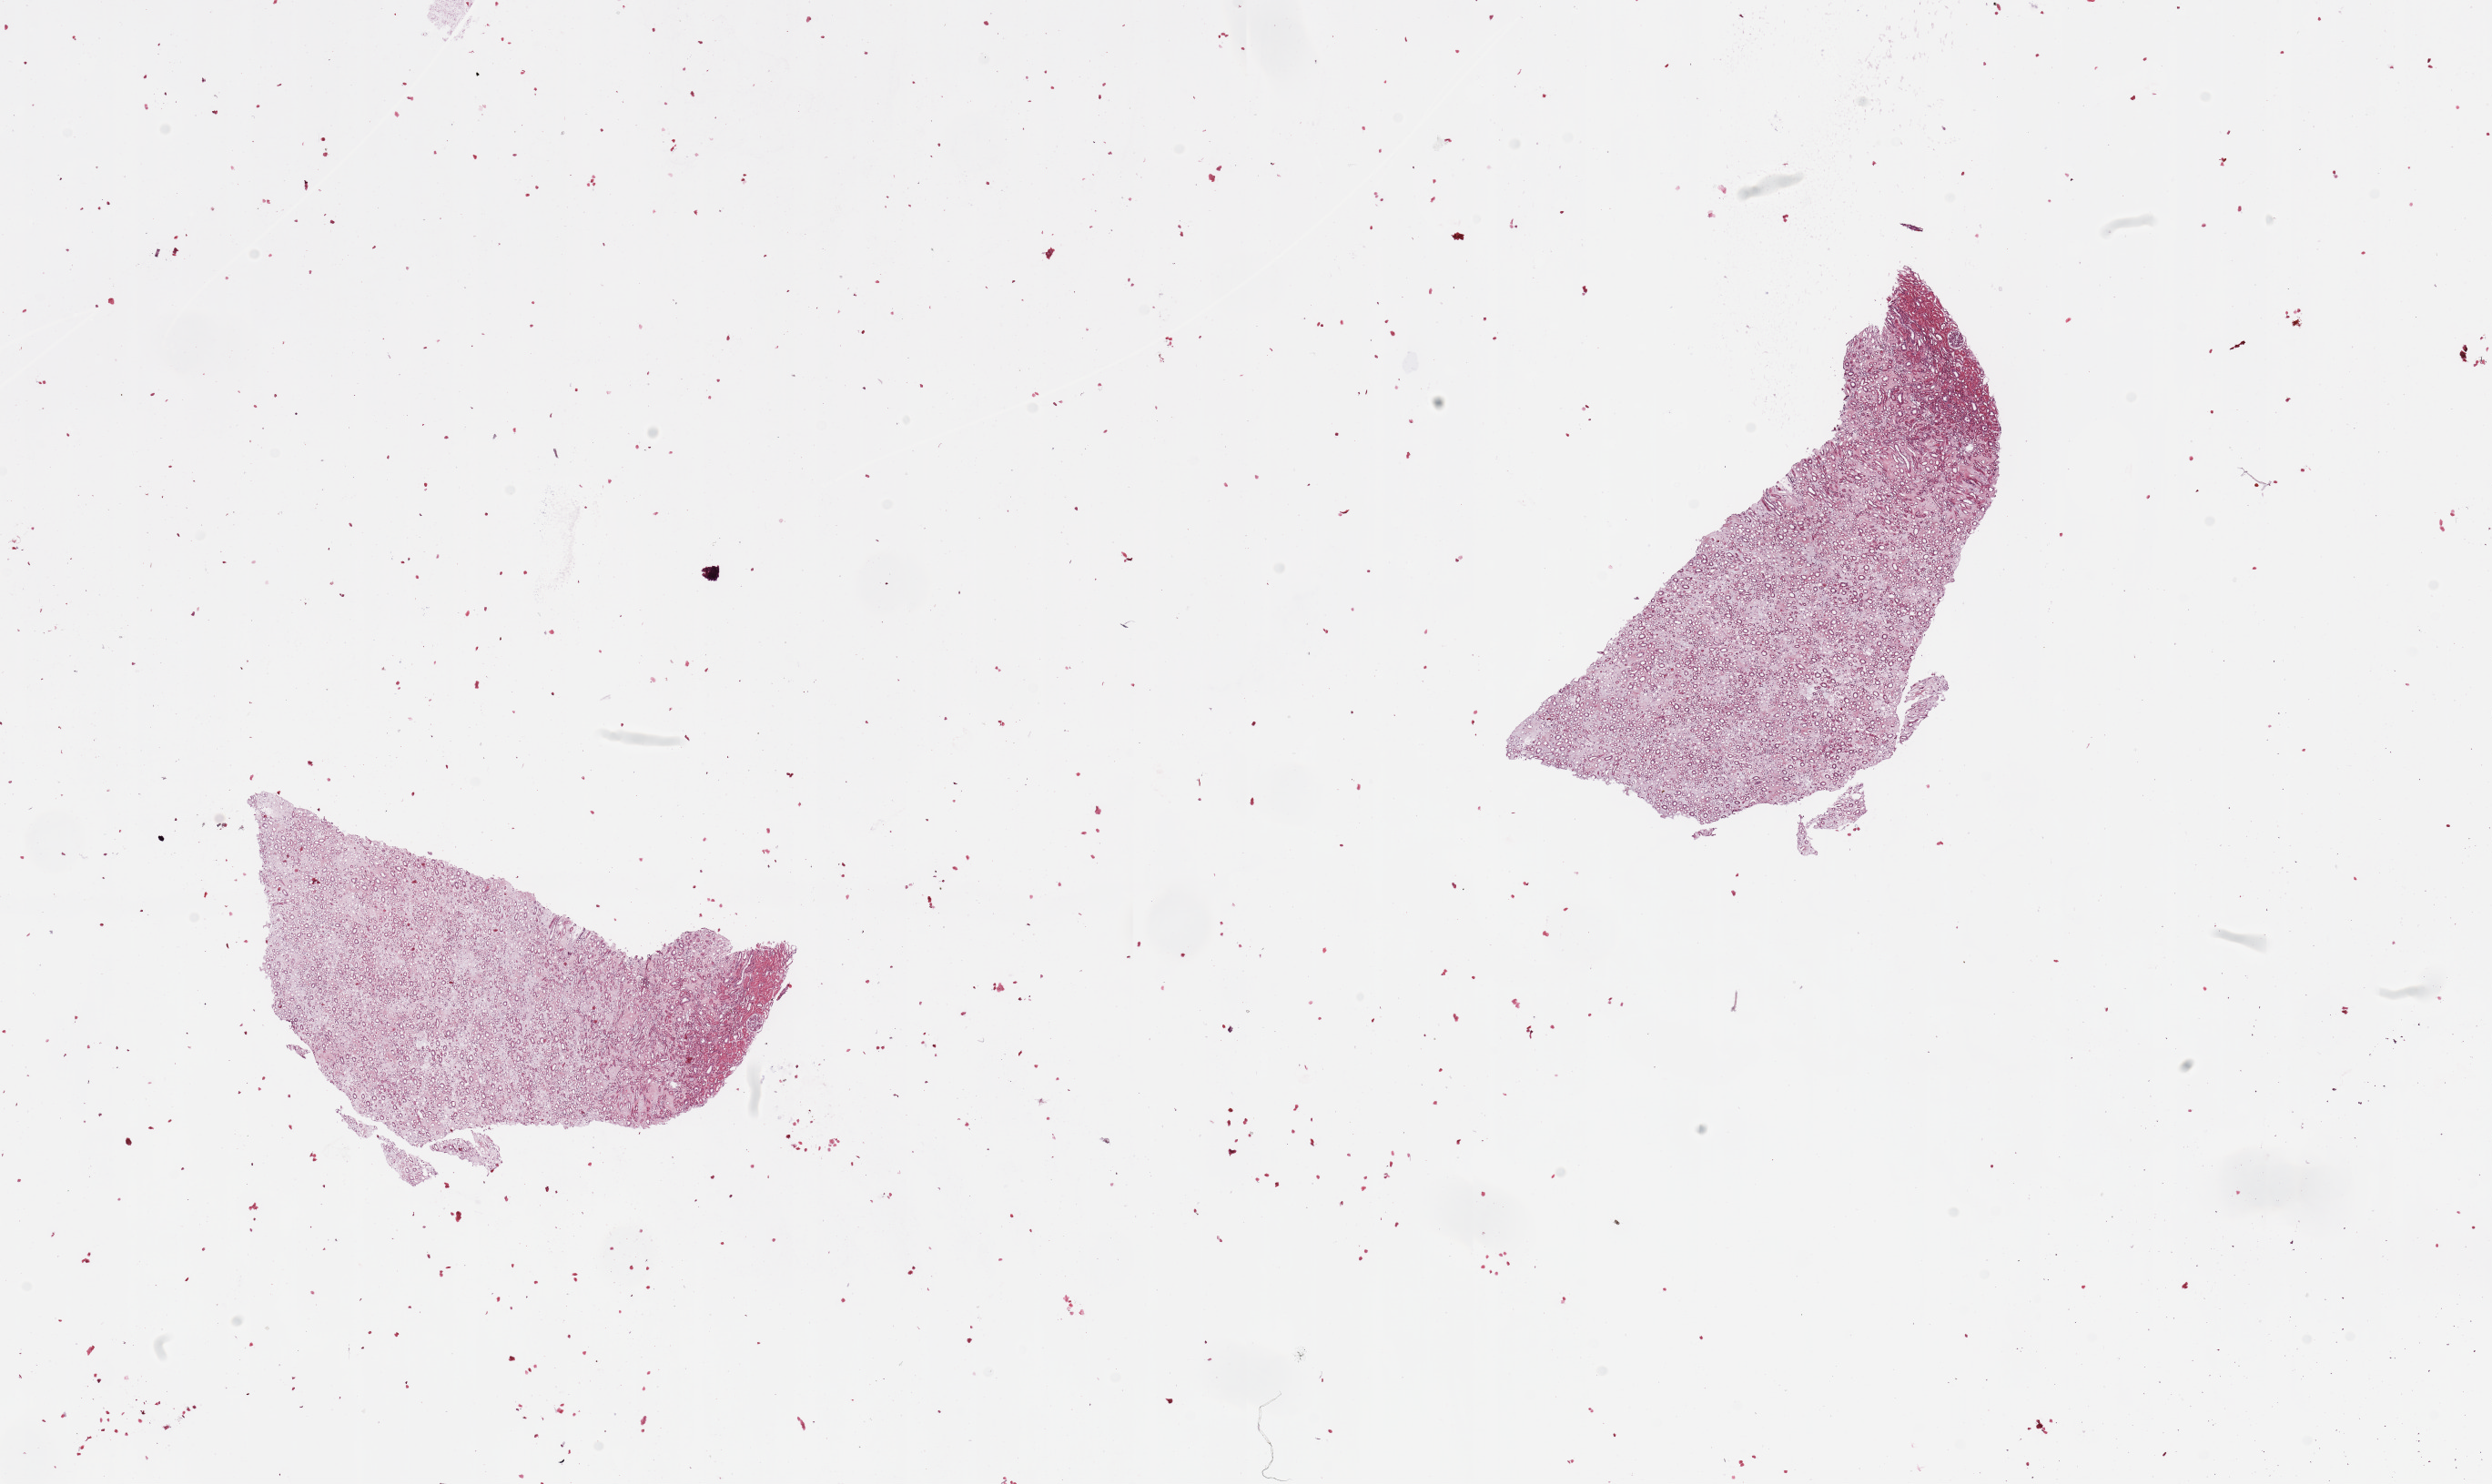
Digitized H&E tissue section (whole slide) — shown as a low-resolution overview of the whole scanned area (about 21.7 x 12.9 mm); normal (non-tumour) tissue sample, sampled site: kidney. Patient: male, age 69 years.
• this section: normal (non-tumour) tissue from the same patient
• patient diagnosis: Renal cell carcinoma, NOS